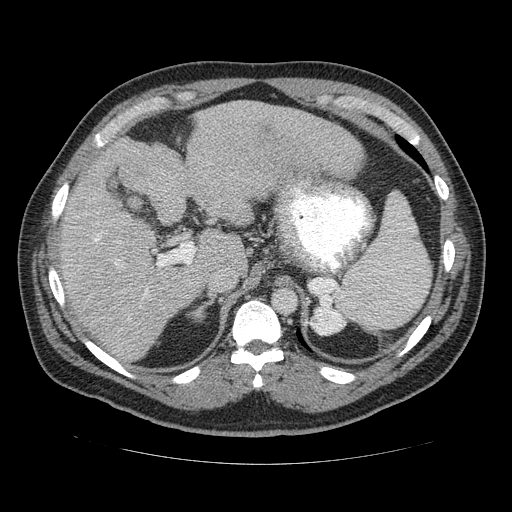
Contrast-enhanced abdominal CT (liver protocol), one axial slice. Position 87 of 113 along the scan axis. Reconstruction kernel STANDARD. Soft-tissue window (W 400 / L 40 HU). 2.5 mm slice thickness. 512 × 512 image matrix. From the clinical record (not read from this slice): diagnosis: hepatocellular carcinoma (patient treated with transarterial chemoembolisation; whether this scan precedes or follows treatment is not stated here); TNM stage (as recorded): Stage-II; Child-Pugh class: B; tumour differentiation: moderately differentiated; tumour nodularity: multinodular.
Outlined on this slice (semi-automatic segmentation, software-assisted and operator-edited):
- liver parenchyma outside the tumour (the mass and vessels are separate outlines, so this box may not span the whole liver): bounding box [x1, y1, x2, y2] px = [50, 102, 368, 362]
- liver vessels: [94, 199, 211, 316]